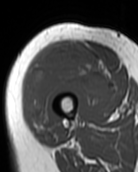
MRI of an extremity soft-tissue mass, one axial slice; slice 33 of 99 in the series (ordered by position); MR volume resampled by the dataset authors to the PET/CT grid (not the native acquisition matrix); 138 × 172 image matrix, field of view 135 × 168 mm. Female patient. From the clinical record (not read from this slice): histological type: pleiomorphic undifferentiated sarcoma; grade: high; site of the primary tumour: right quadricep.
Annotated regions visible in this slice (expert contour drawn on MRI and transferred to this co-registered scan by the dataset authors):
- gross tumour volume including surrounding oedema: box from (x=25, y=48) to (x=109, y=131) px
- gross tumour volume (mass): (x=25, y=48)–(x=109, y=131)